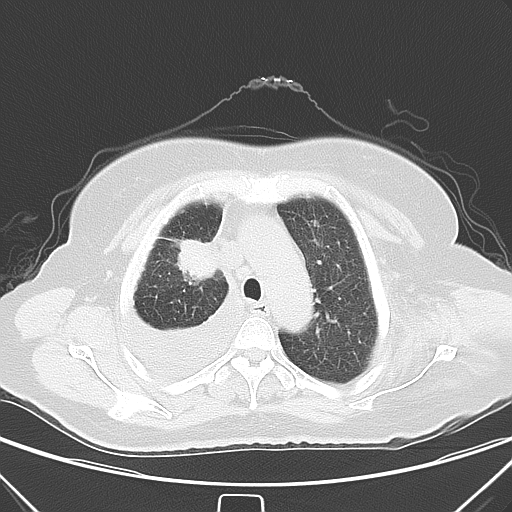
Chest CT, one axial slice; slice 44 of 55 in the series (ordered by position); lung window (W 1500 / L -600 HU); 512 × 512 image matrix. Patient: female, 66 years. From the clinical record (not read from this slice): clinical TNM (as recorded): T2 N0 M1.
Structures marked on this image (bounding box drawn by a radiologist):
- lung tumour (recorded histology: adenocarcinoma): bounding box [x1, y1, x2, y2] px = [171, 236, 218, 285]